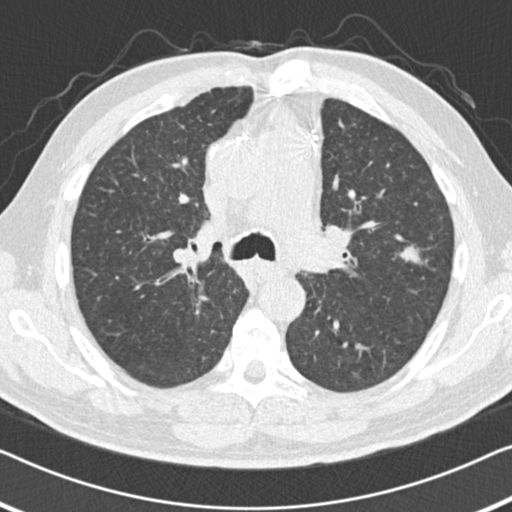
Low-dose screening chest CT, one axial slice; position 101 of 155 along the scan axis; reconstruction kernel B30f; 120 kVp; lung window (W 1500 / L -600 HU); 2 mm slice thickness; 512 × 512 image matrix.
Outlined on this slice (outlined manually by an expert reader):
- lesion 1 (tumor, upper lobe of left lung): bounding box [x1, y1, x2, y2] px = [399, 244, 420, 264]